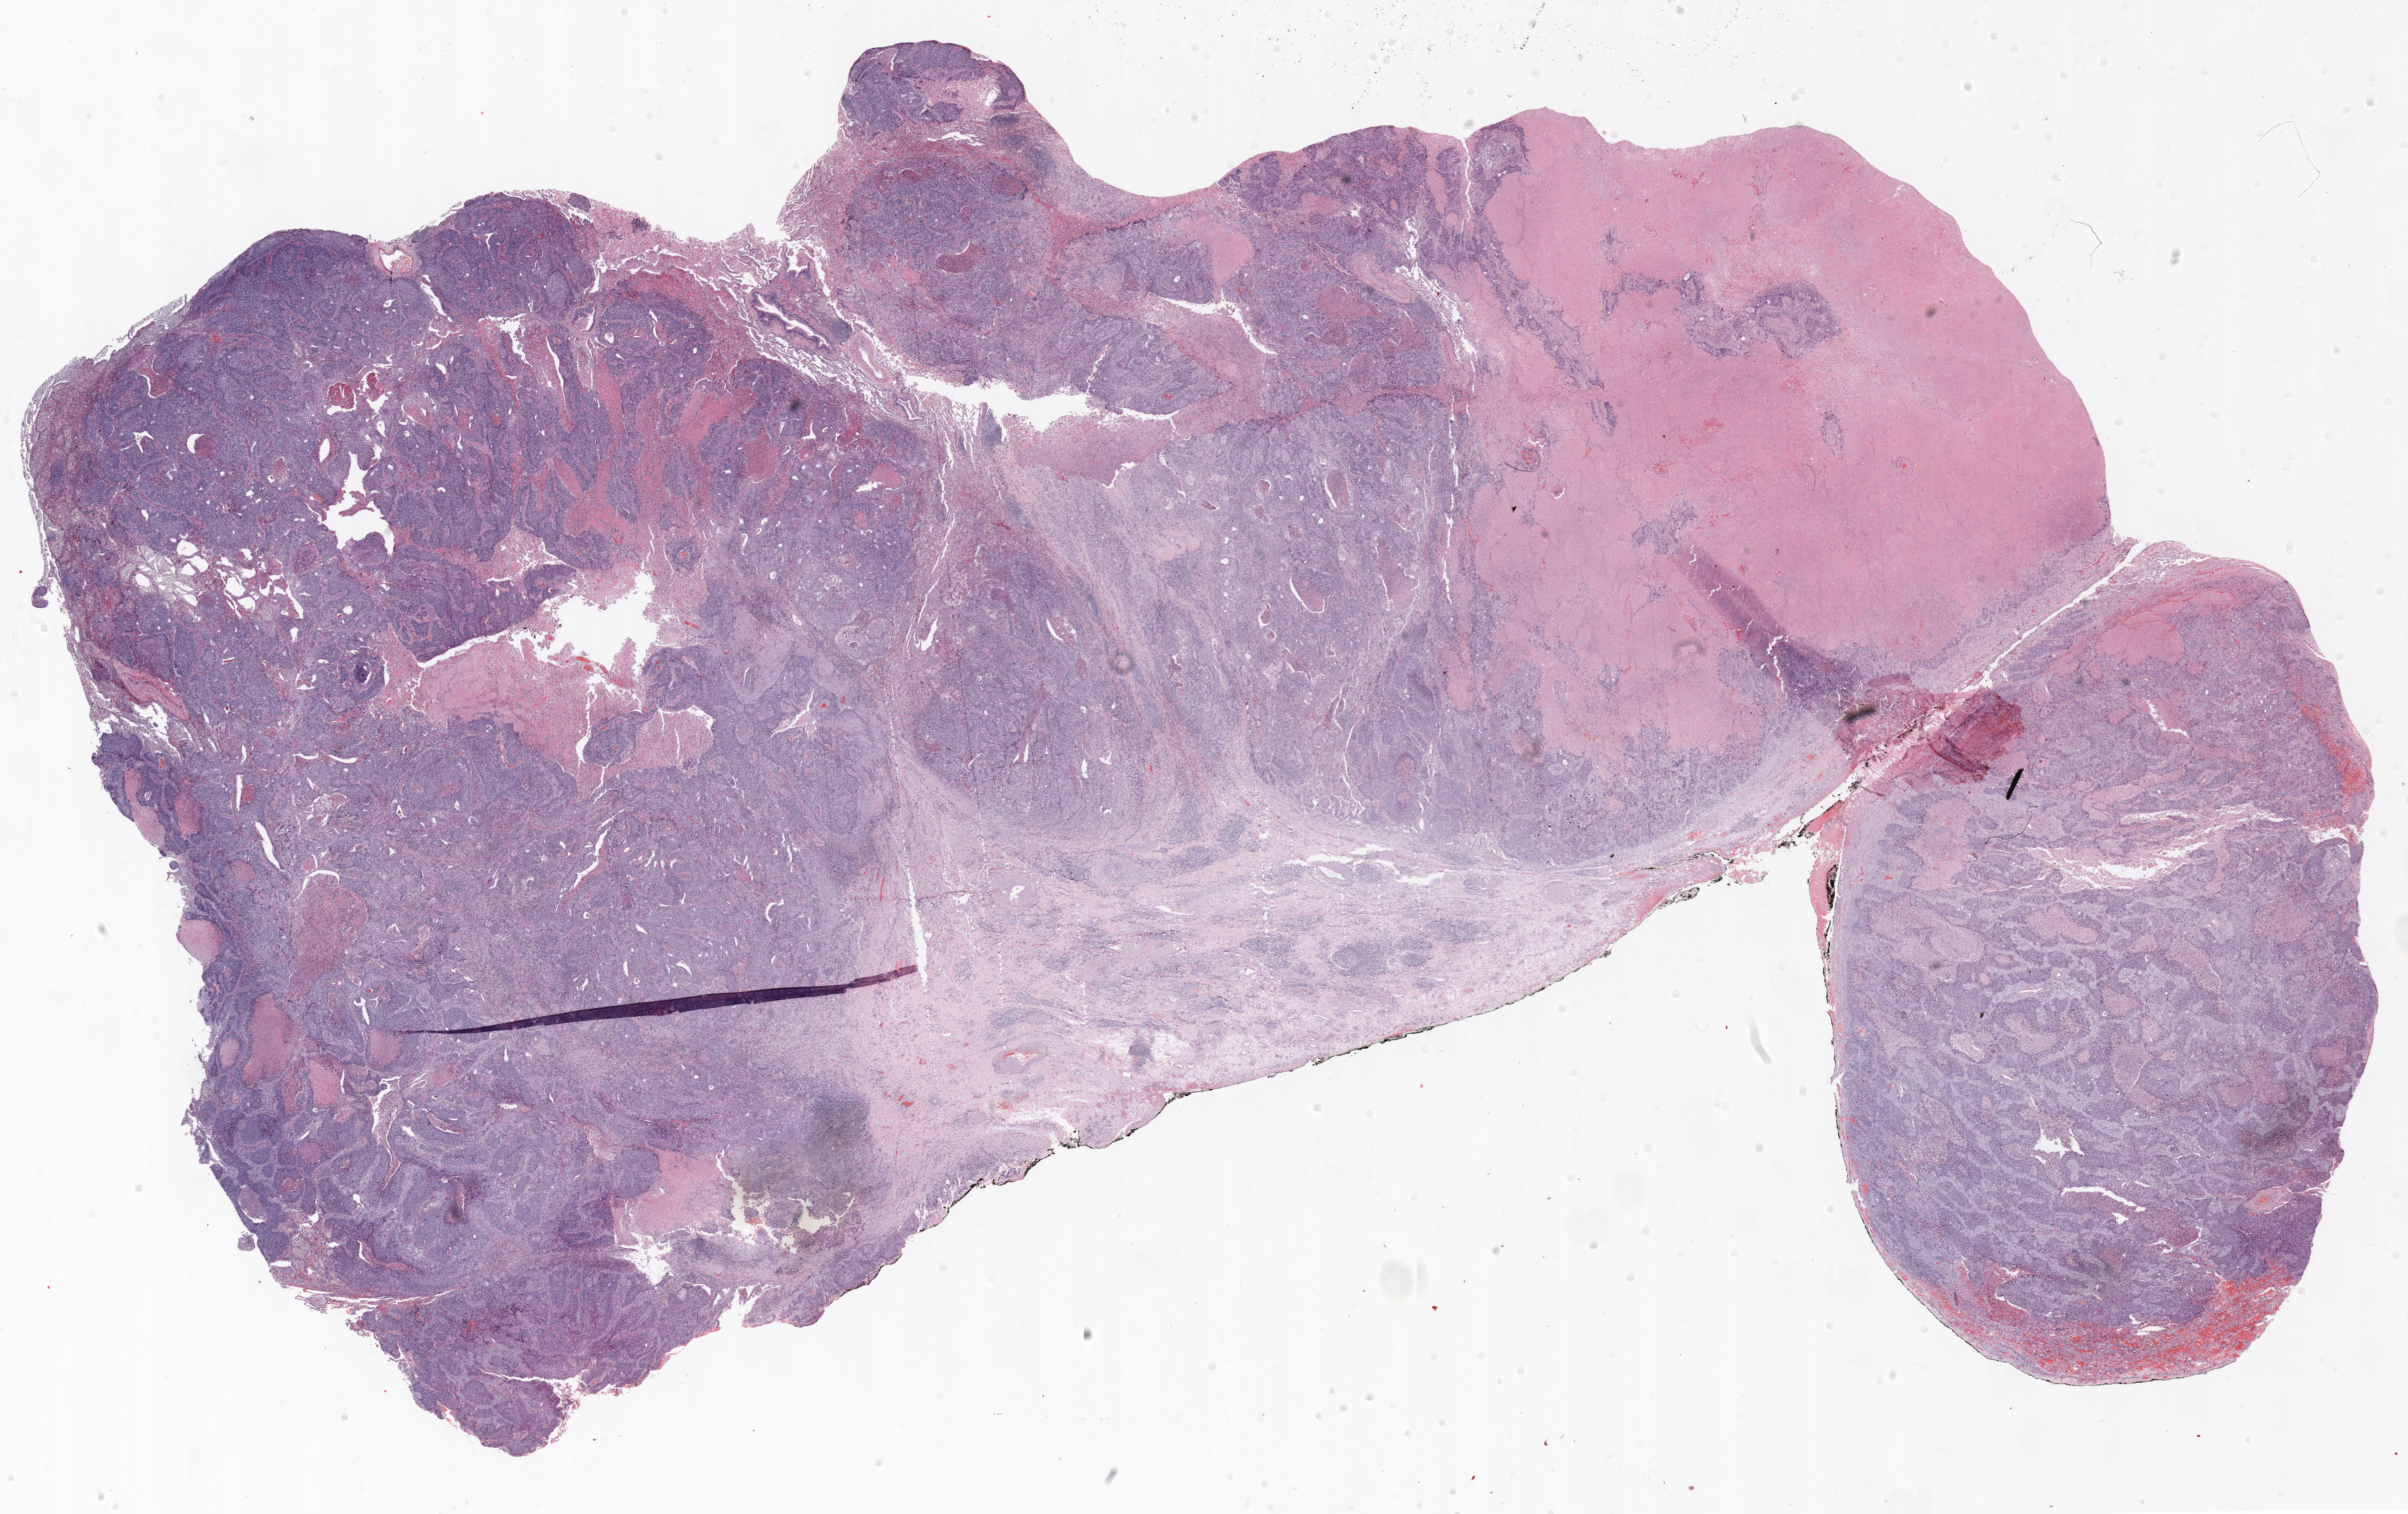
Whole-slide histology image, H&E-stained — a low-resolution overview of the entire scanned area, about 29.0 x 18.3 mm, formalin-fixed paraffin-embedded (FFPE) section, lung tissue. Male patient, aged 60 at enrolment. Current smoker at enrolment. Grade: moderately differentiated (G2).
* stage (AJCC 6th edition): IB
* tumour size (pathology): 50 mm
* ICD-O-3 topography: lower lobe of lung (C34.3)
* participant's lung-cancer diagnosis: Squamous cell carcinoma, NOS
* primary tumour location (clinical record): right lower lobe